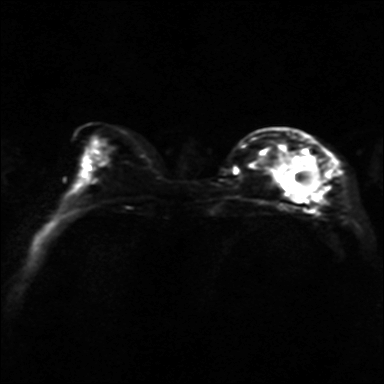
Breast MRI, one axial slice. Position 13 of 36 along the scan axis. Diffusion-weighted series; image 2 of 4 stored at this slice position (different b-values; order by instance number). 3 T. 4 mm slice thickness. 384 × 384 image matrix, field of view 320 × 320 mm. Female patient.
Annotated regions visible in this slice (outlined manually by an expert reader):
- tumour on diffusion-weighted imaging: box from (x=285, y=157) to (x=320, y=199) px